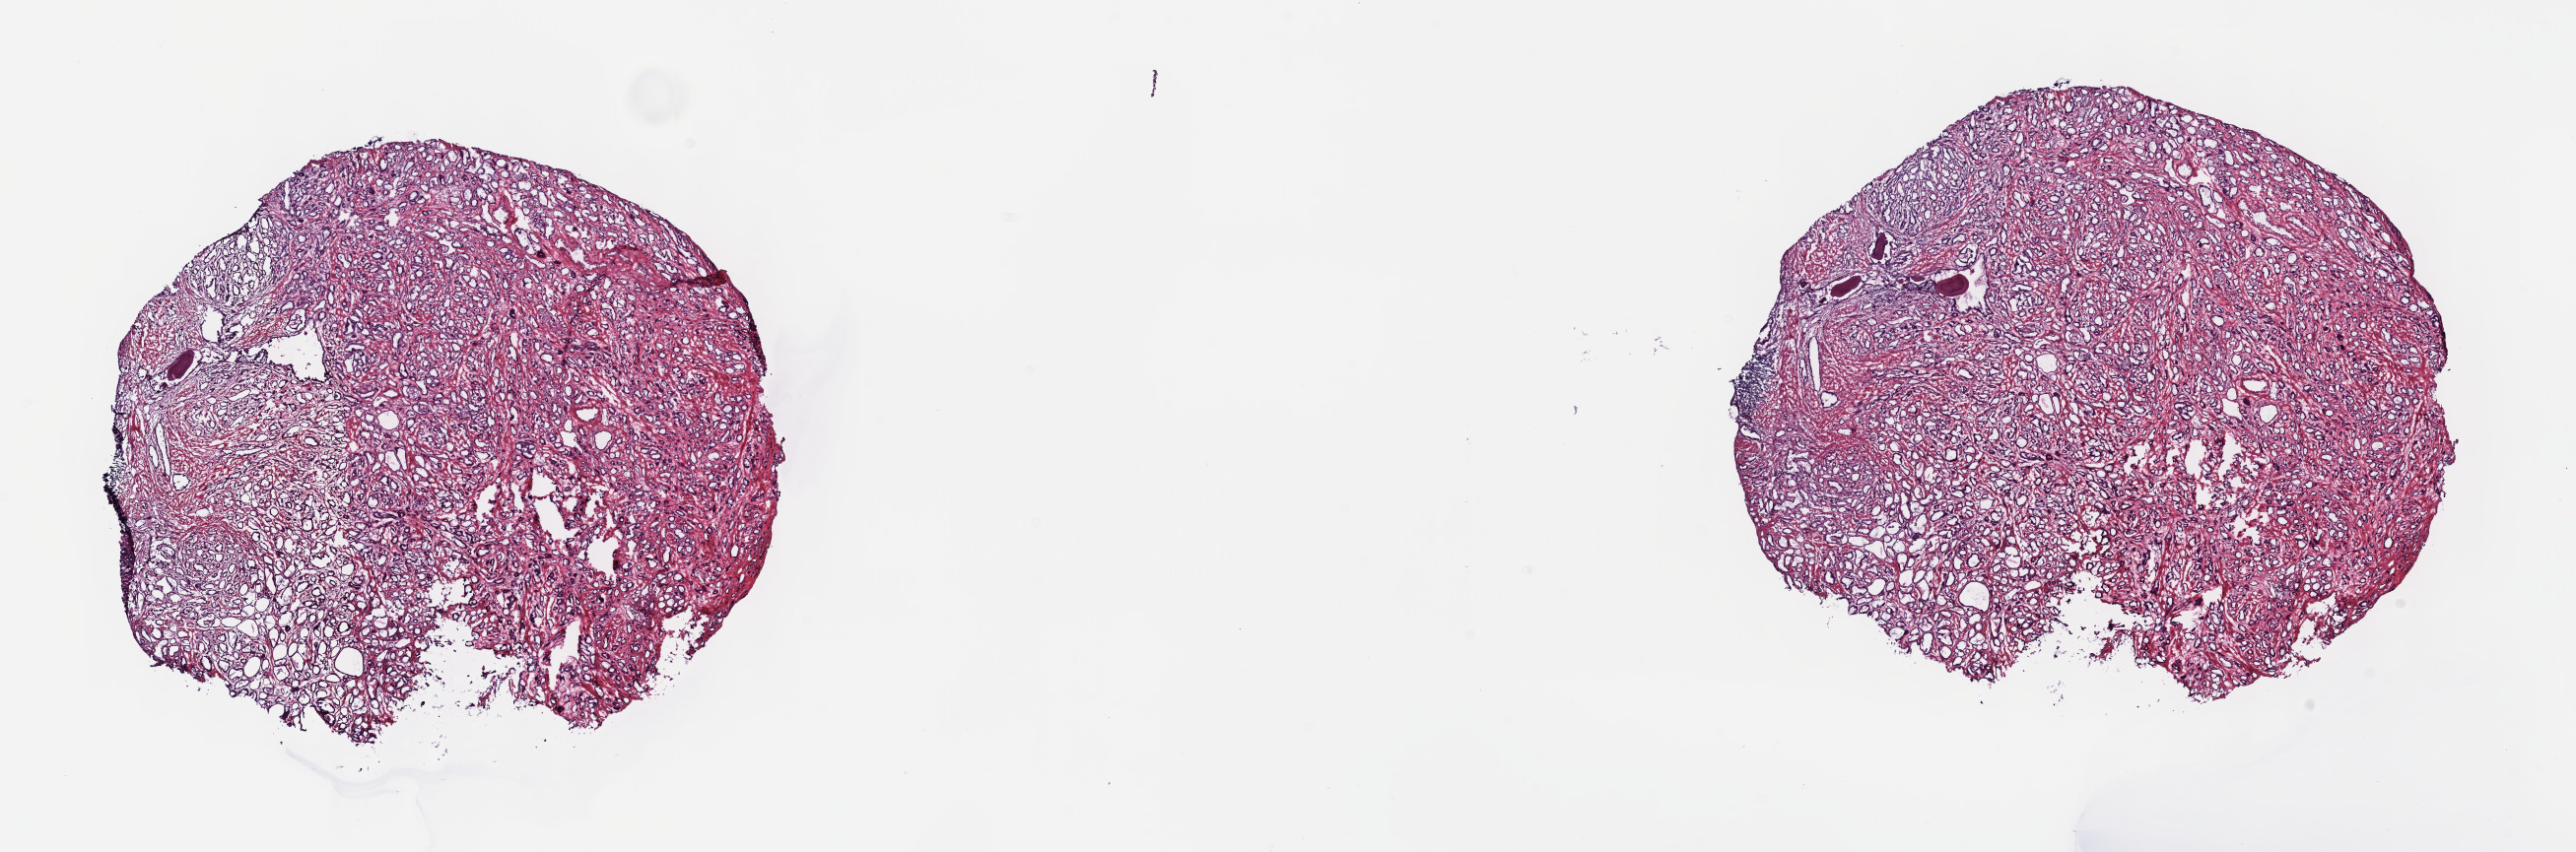
Digitized H&E-stained tissue section (whole slide), low-resolution overview of the scanned area, about 21.1 x 7.0 mm. Frozen section from the top of the tissue portion. Sample: primary tumour, prostate. Patient: male, age at initial diagnosis 56 years. Gleason score: 6 (3+3). Composition of this section per pathologist review: tumour cells 80%, tumour nuclei 80%, normal cells 0%, stromal cells 20%, necrosis 0%. Inflammatory infiltration, as recorded: lymphocyte infiltration 40%, monocyte infiltration 20%, neutrophil infiltration 20%.
Pathologic diagnosis: Adenocarcinoma, NOS. Lymph nodes positive (case pathology): 0 of 28 examined. Laterality: left.